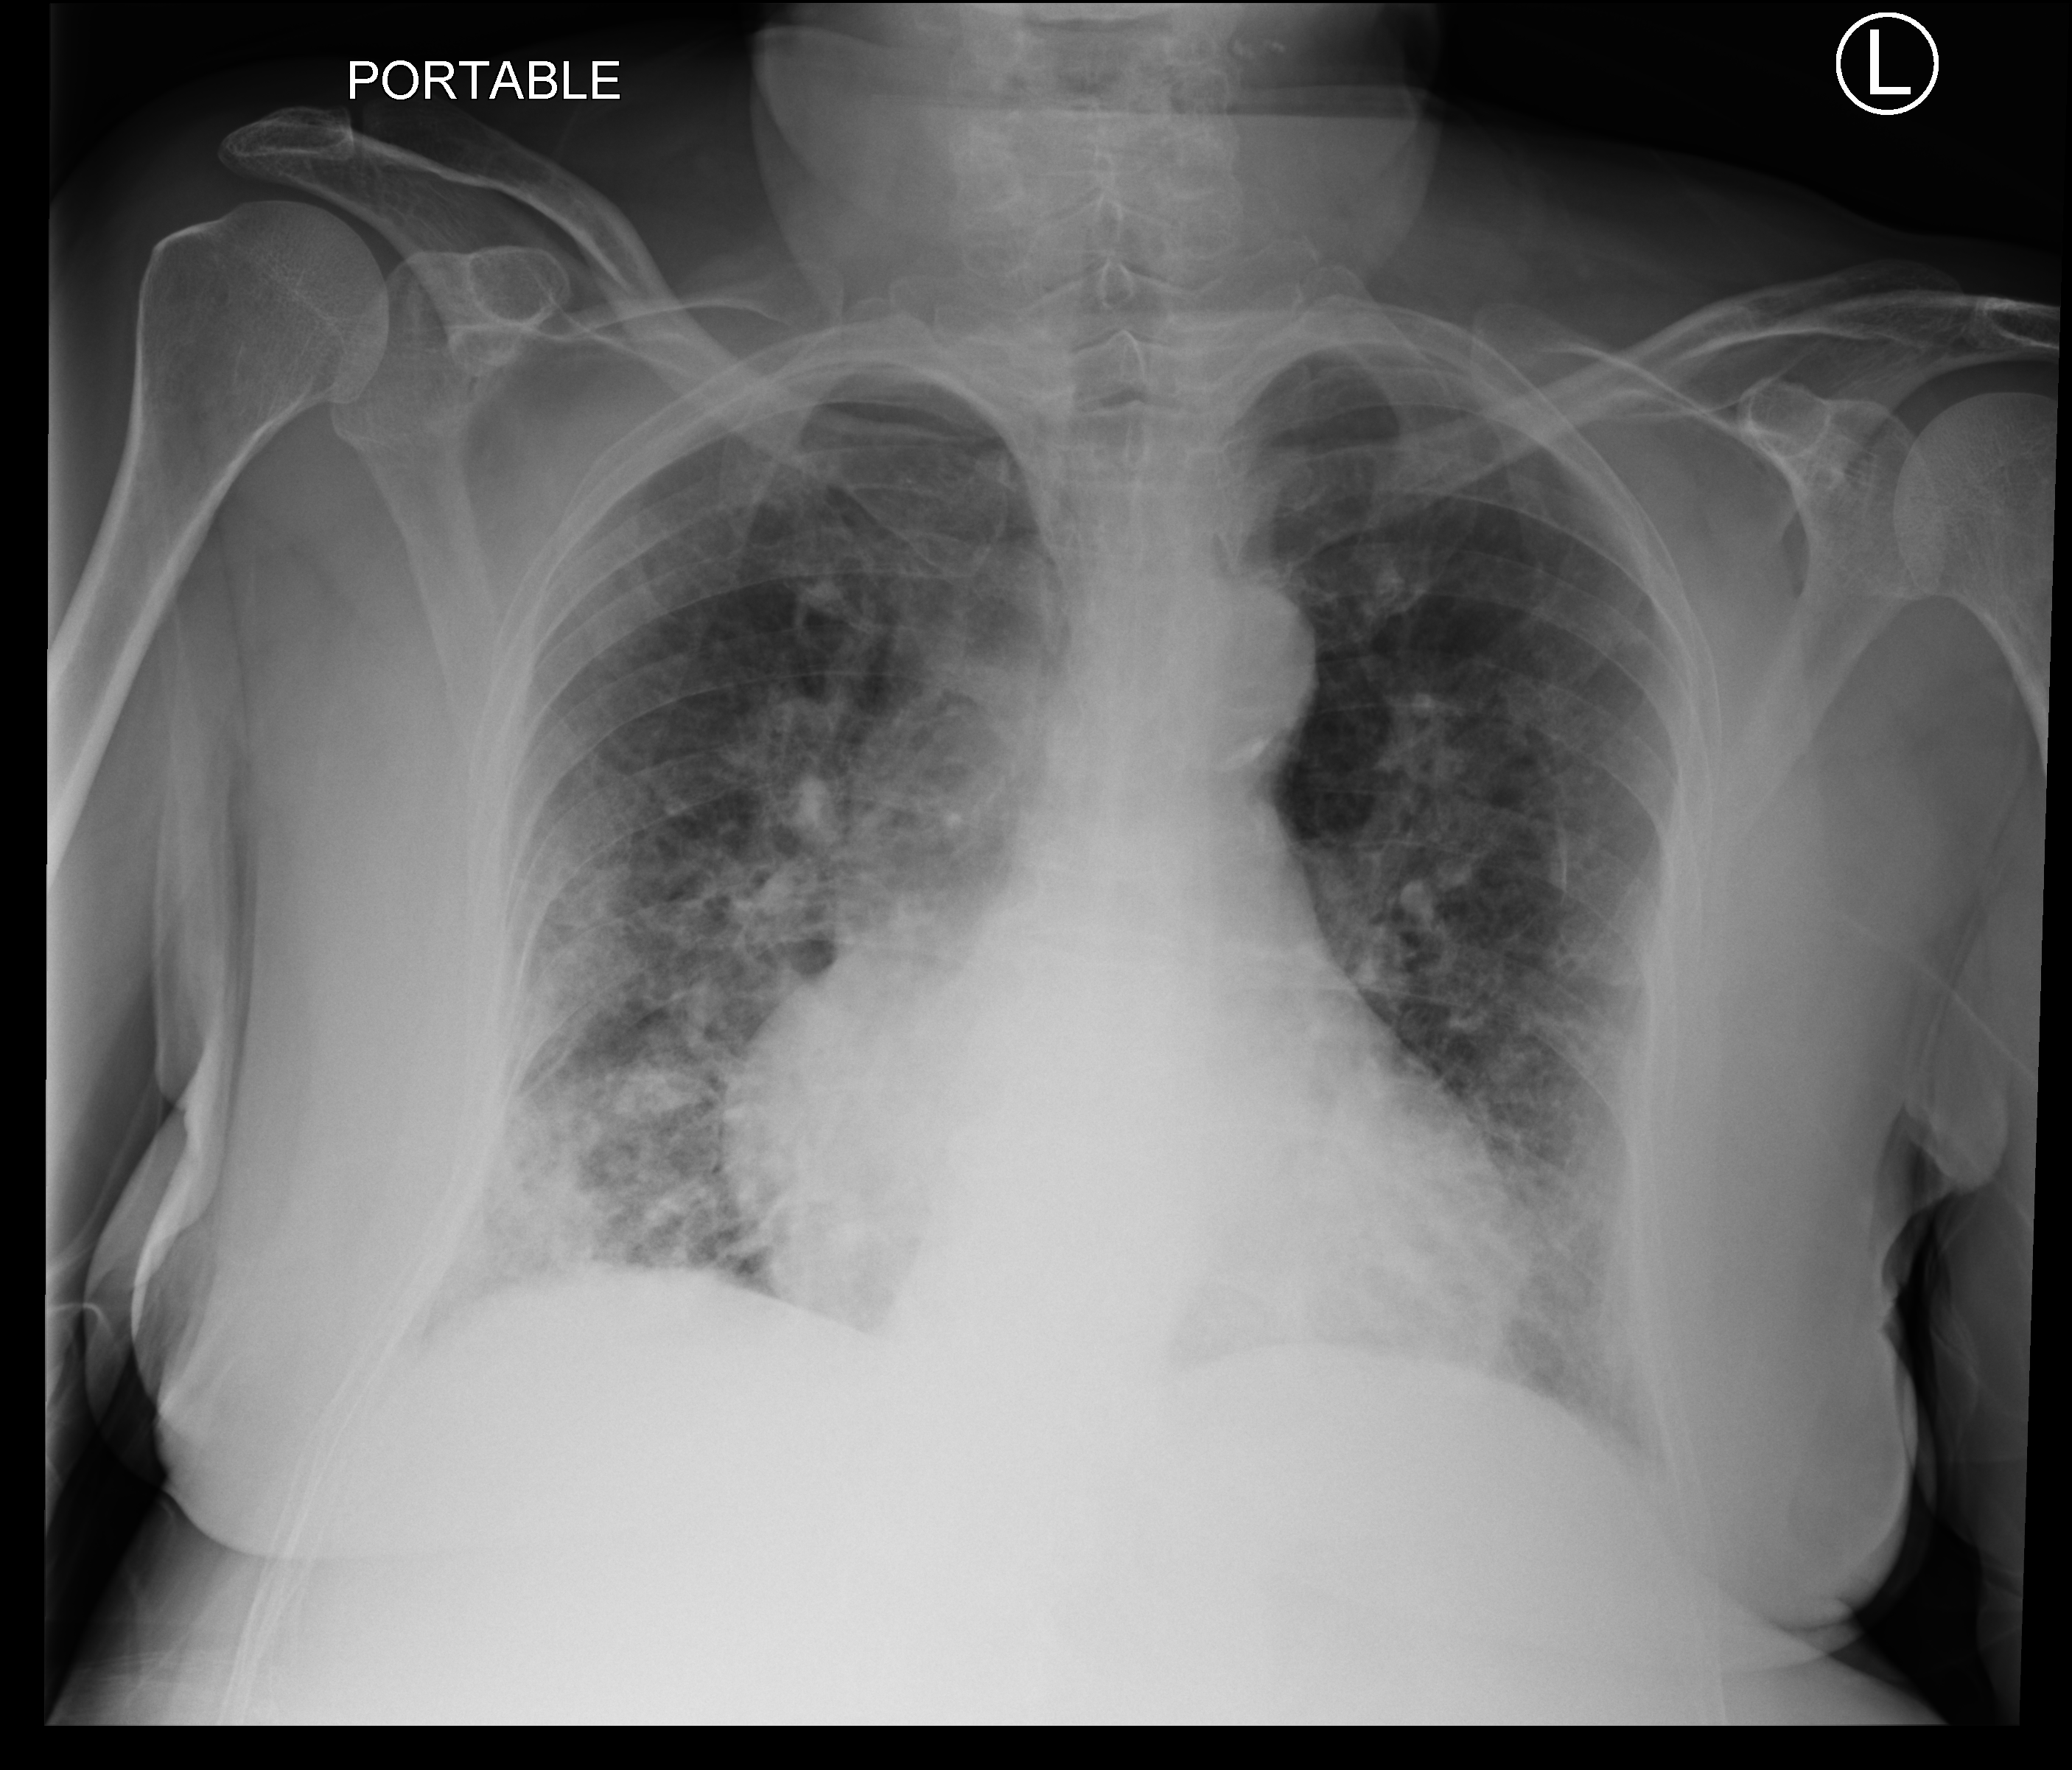
Portable chest radiograph. Patient hospitalised with COVID-19; female, aged 75–90 years.
Admission-level facts for this patient (not findings on this image; timing relative to this image not recorded):
- mechanically ventilated during this hospital stay: yes
- other chronic lung disease (admission record): yes
- admitted to intensive care during this hospital stay: yes